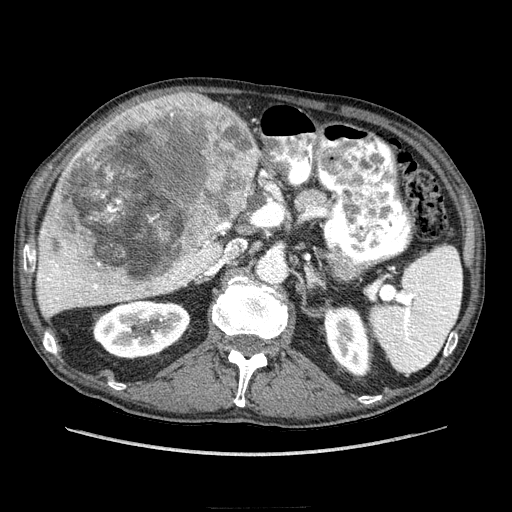
Contrast-enhanced abdominal CT (liver protocol), one axial slice. Slice 135 of 218 in the series (ordered by position). Reconstruction kernel STANDARD. 100 kVp. Soft-tissue window (W 400 / L 40 HU). 2.5 mm slice thickness. 512 × 512 image matrix. From the clinical record (not read from this slice): diagnosis: hepatocellular carcinoma (patient treated with transarterial chemoembolisation; whether this scan precedes or follows treatment is not stated here); TNM stage (as recorded): Stage-IIIA; Child-Pugh class: A; tumour differentiation: well differentiated; tumour nodularity: multinodular.
Outlined on this slice (semi-automatically segmented with operator editing):
- liver parenchyma outside the tumour (the mass and vessels are separate outlines, so this box may not span the whole liver): bounding box (x1, y1, x2, y2) in pixels: (36, 102, 258, 316)
- mass: (40, 91, 258, 290)
- liver vessels: (38, 266, 184, 307)